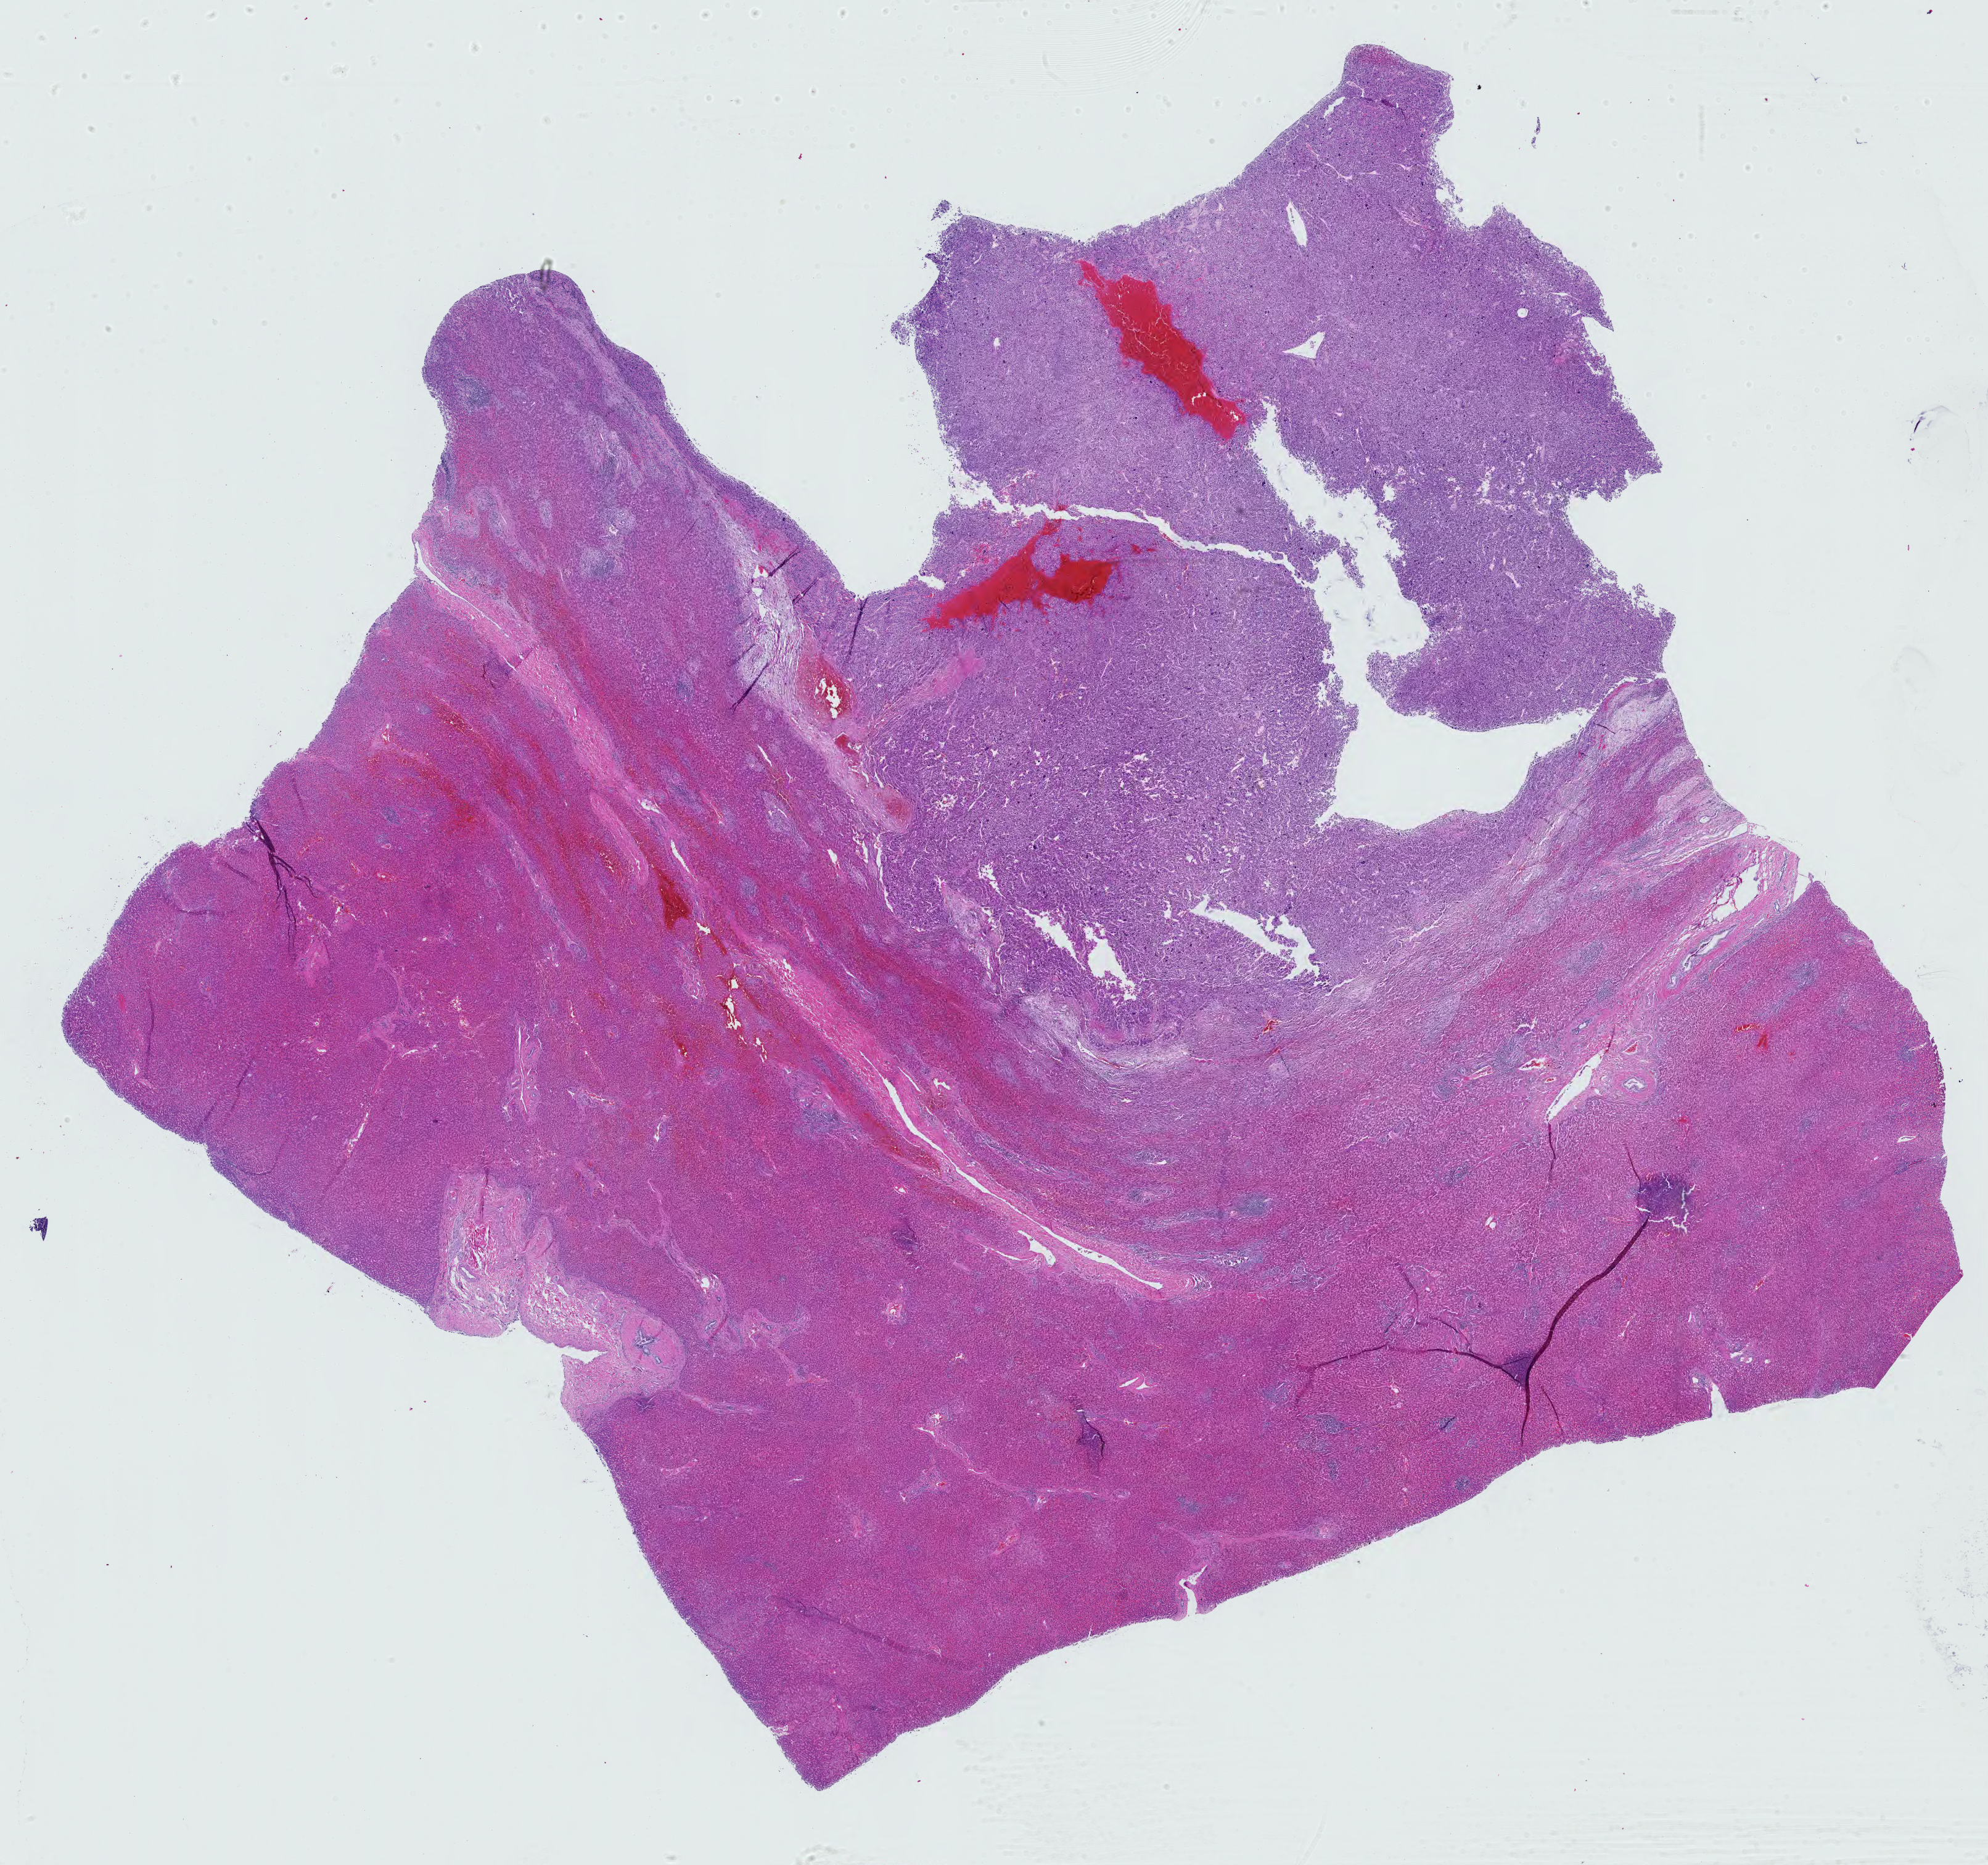
Digitized Hematoxylin and eosin (H&E) stained tissue section (whole slide) — low-resolution overview of the scanned area, about 23.4 x 21.9 mm; FFPE section; sample: primary tumour, liver. Male patient; age at initial diagnosis 48 years. Histologic grade: G2 (moderately differentiated).
* AJCC pathologic stage: II (7th edition)
* diagnosis: Hepatocellular carcinoma, NOS